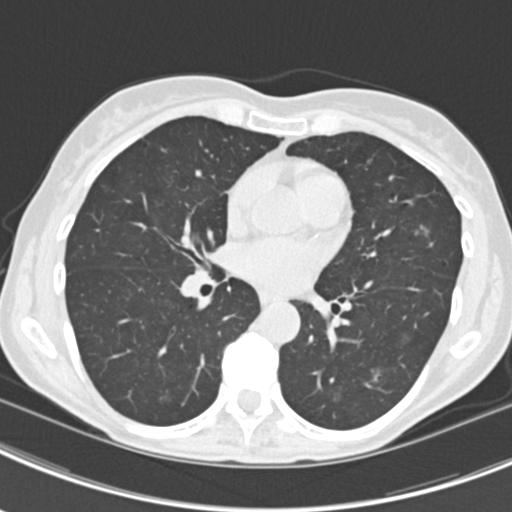
Low-dose screening chest CT, axial slice; second screening round (one year after baseline); lung window (W 1500 / L -600 HU); 2 mm slice thickness; slice 98 of 219 in the series; 512 × 512 image matrix. Female participant, aged 63 years at enrolment. Current smoker at enrolment.
Lesion marked by an expert reader, bounding box (x1, y1, x2, y2) in pixels: (398, 213, 435, 252). The screening reader recorded 9 non-calcified nodules or masses ≥4 mm on this exam (left upper lobe, right upper lobe, left upper lobe, left lower lobe, right middle lobe, left lower lobe, left lower lobe, right lower lobe, right lower lobe); which of them this box marks is not recorded. Official screen result: positive, other. Lung cancer was diagnosed 408 days after this screen (after the third annual screen): bronchiolo-alveolar adenocarcinoma, NOS, right upper lobe, right middle lobe, right lower lobe, left upper lobe, left lower lobe, moderately differentiated (G2), stage IV (AJCC 6th edition).